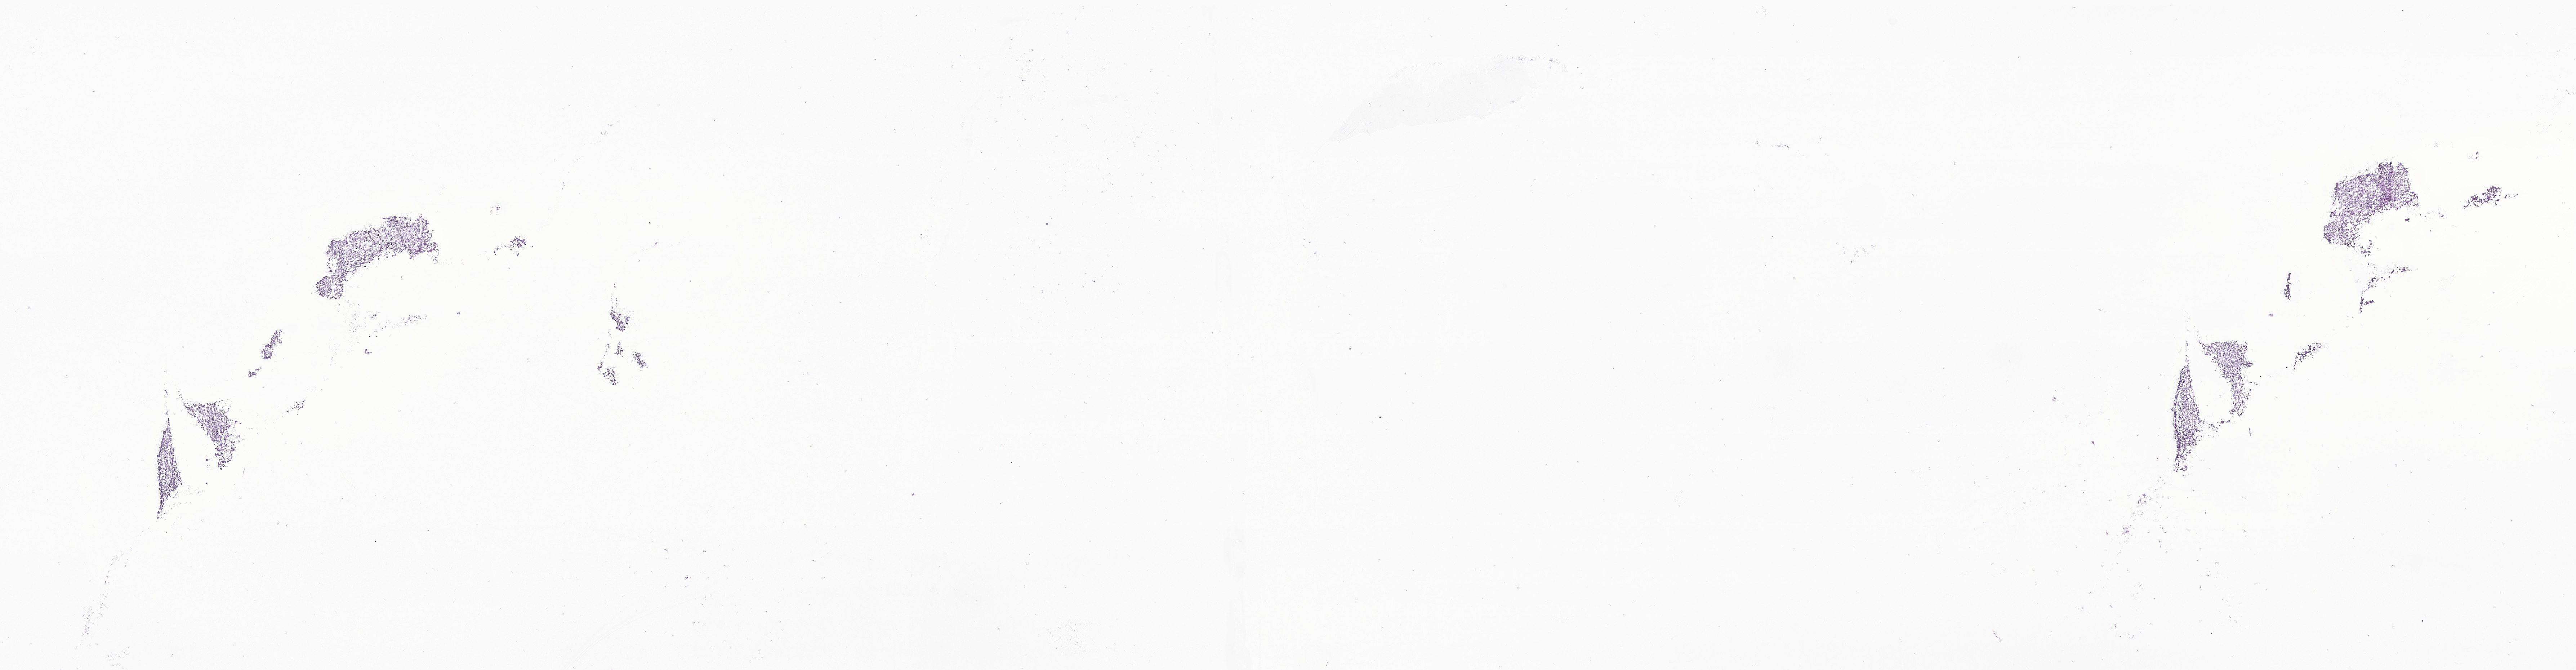
H&E whole-slide image of tumor tissue from the brain, a low-resolution overview of the entire scanned area, about 30.1 x 7.8 mm; frozen section (OCT-embedded). Patient: female, age 142 months (11 years 10 months).
Diagnosis (ICD-O-3 morphology term): Glioma, malignant.